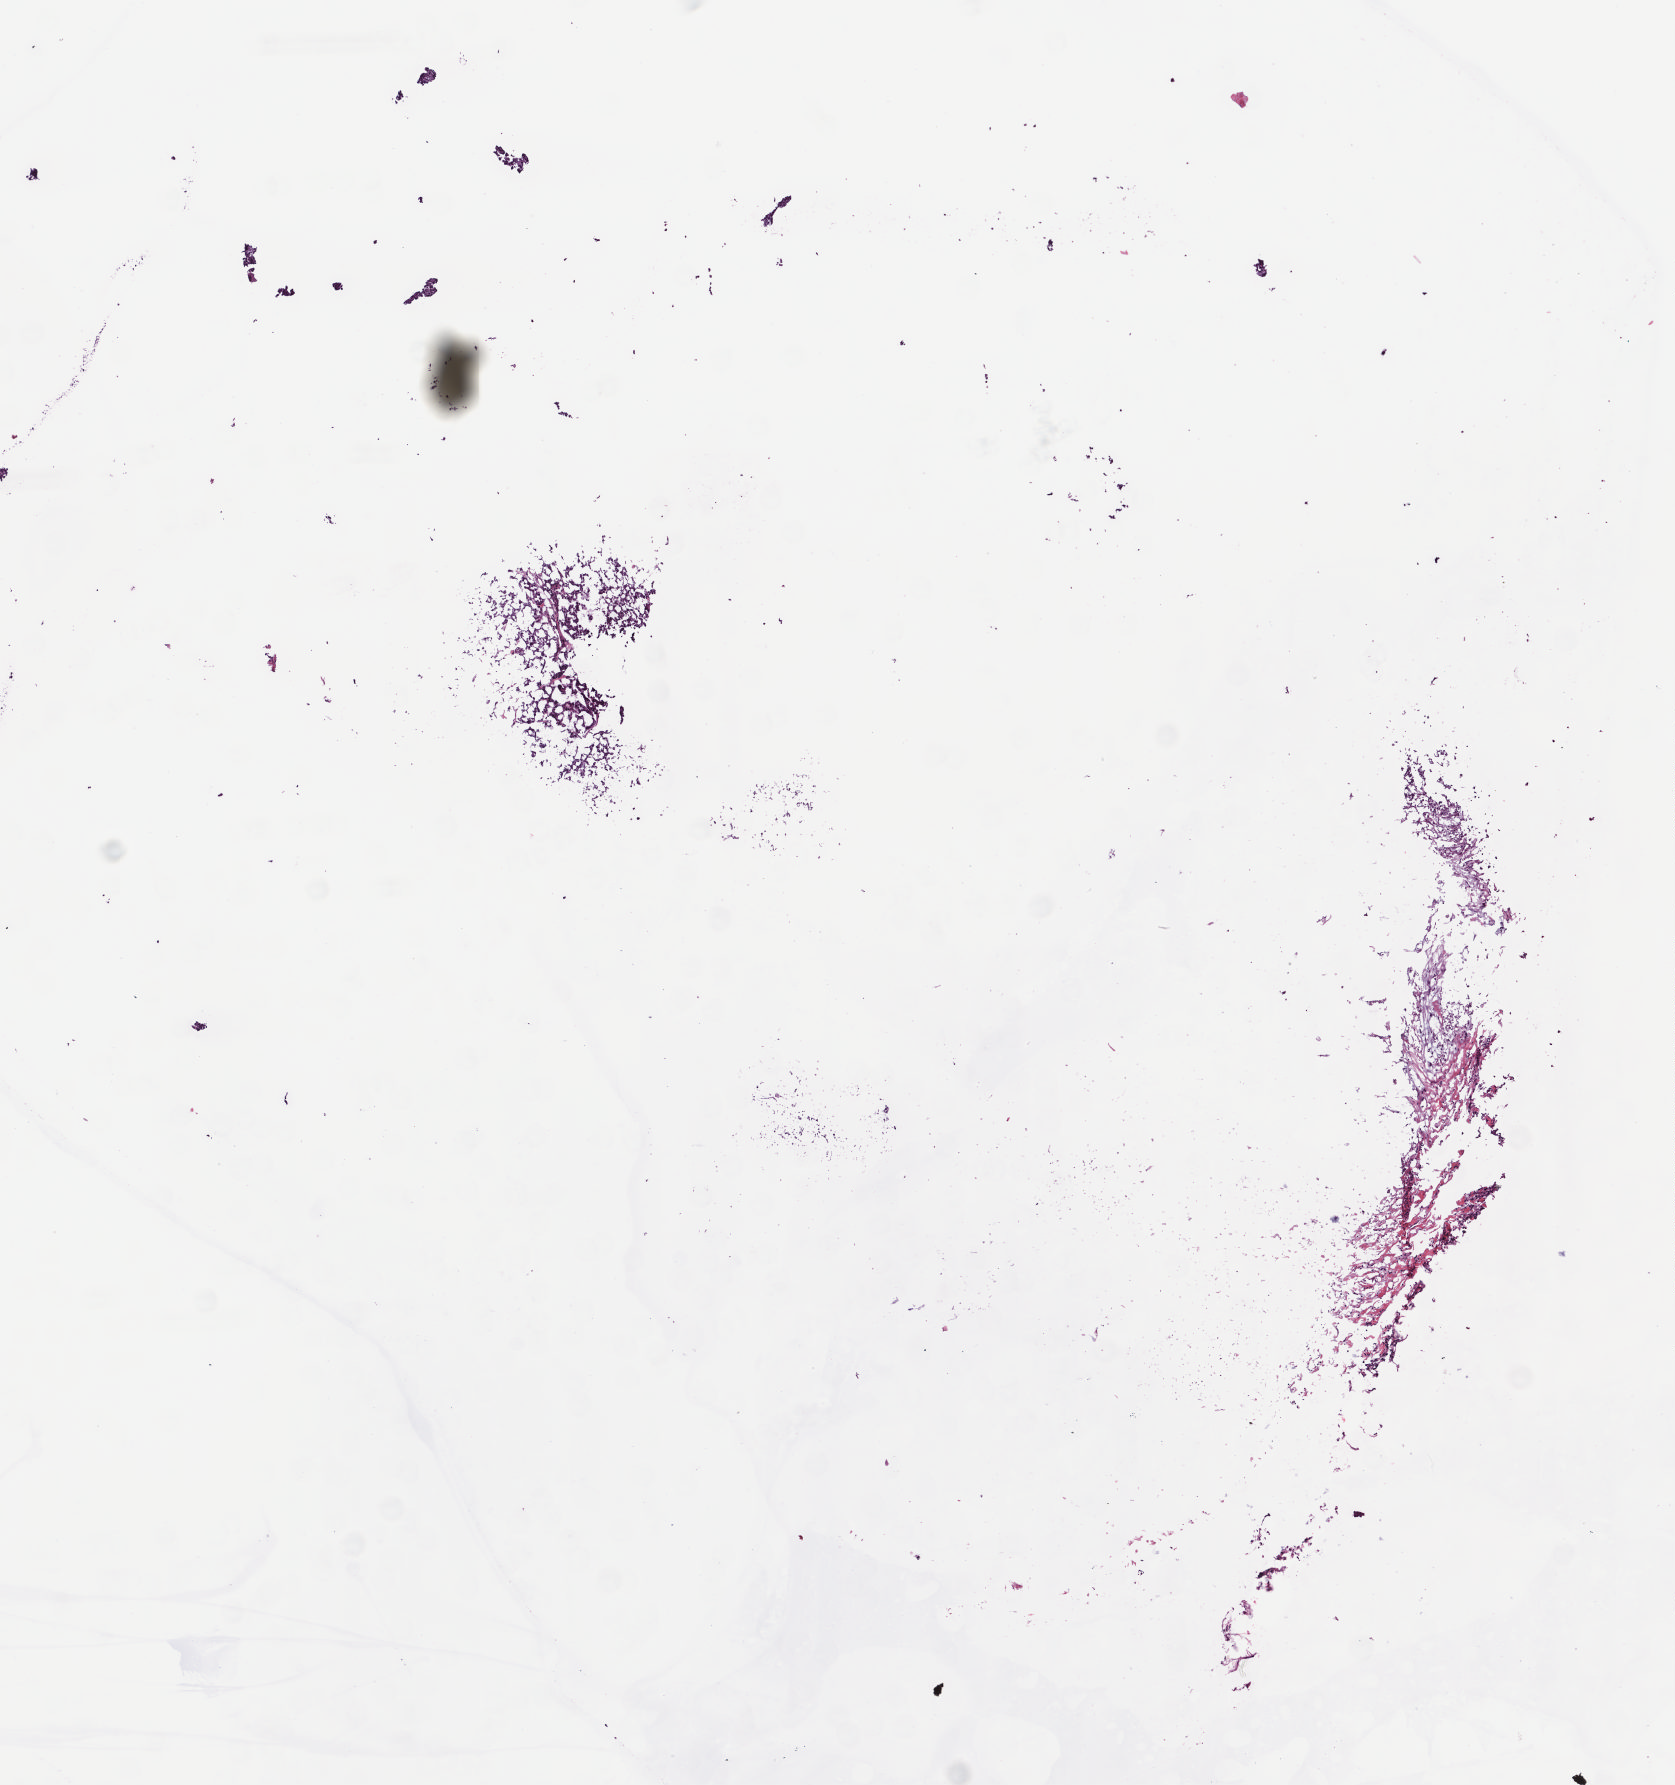
H&E-stained whole-slide image — whole scanned area (about 6.7 x 7.1 mm, acquisition: 40x scan) shown as a low-resolution overview, frozen section from the bottom of the tissue portion, sample: primary tumour, breast. Female patient; age at initial diagnosis 34 years. Slide review estimates, as recorded: tumour cells 80%, tumour nuclei 80%.
Pathologic diagnosis: Infiltrating duct carcinoma, NOS.